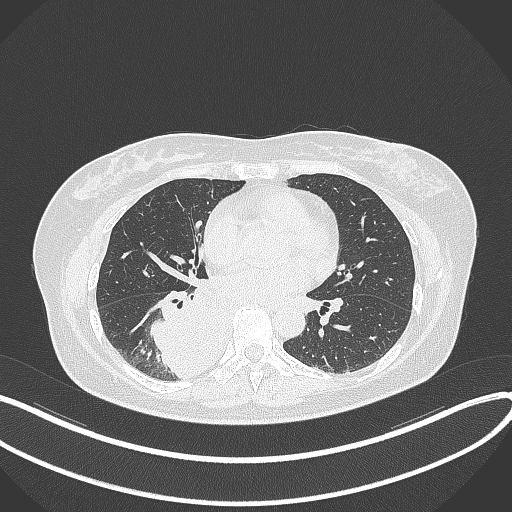
Chest CT, one axial slice. Slice 165 of 331 in the series (ordered by position). Reconstruction kernel B70f. 120 kVp. Lung window (W 1500 / L -600 HU). 512 × 512 image matrix. Patient: female, 54 years. Case-level facts recorded for this patient, not image findings: clinical TNM (as recorded): T4 N0 M0.
Outlined on this slice (bounding box drawn by a radiologist):
- lung tumour (recorded histology: adenocarcinoma): bounding box <148,287,231,383> (left, top, right, bottom; pixels)